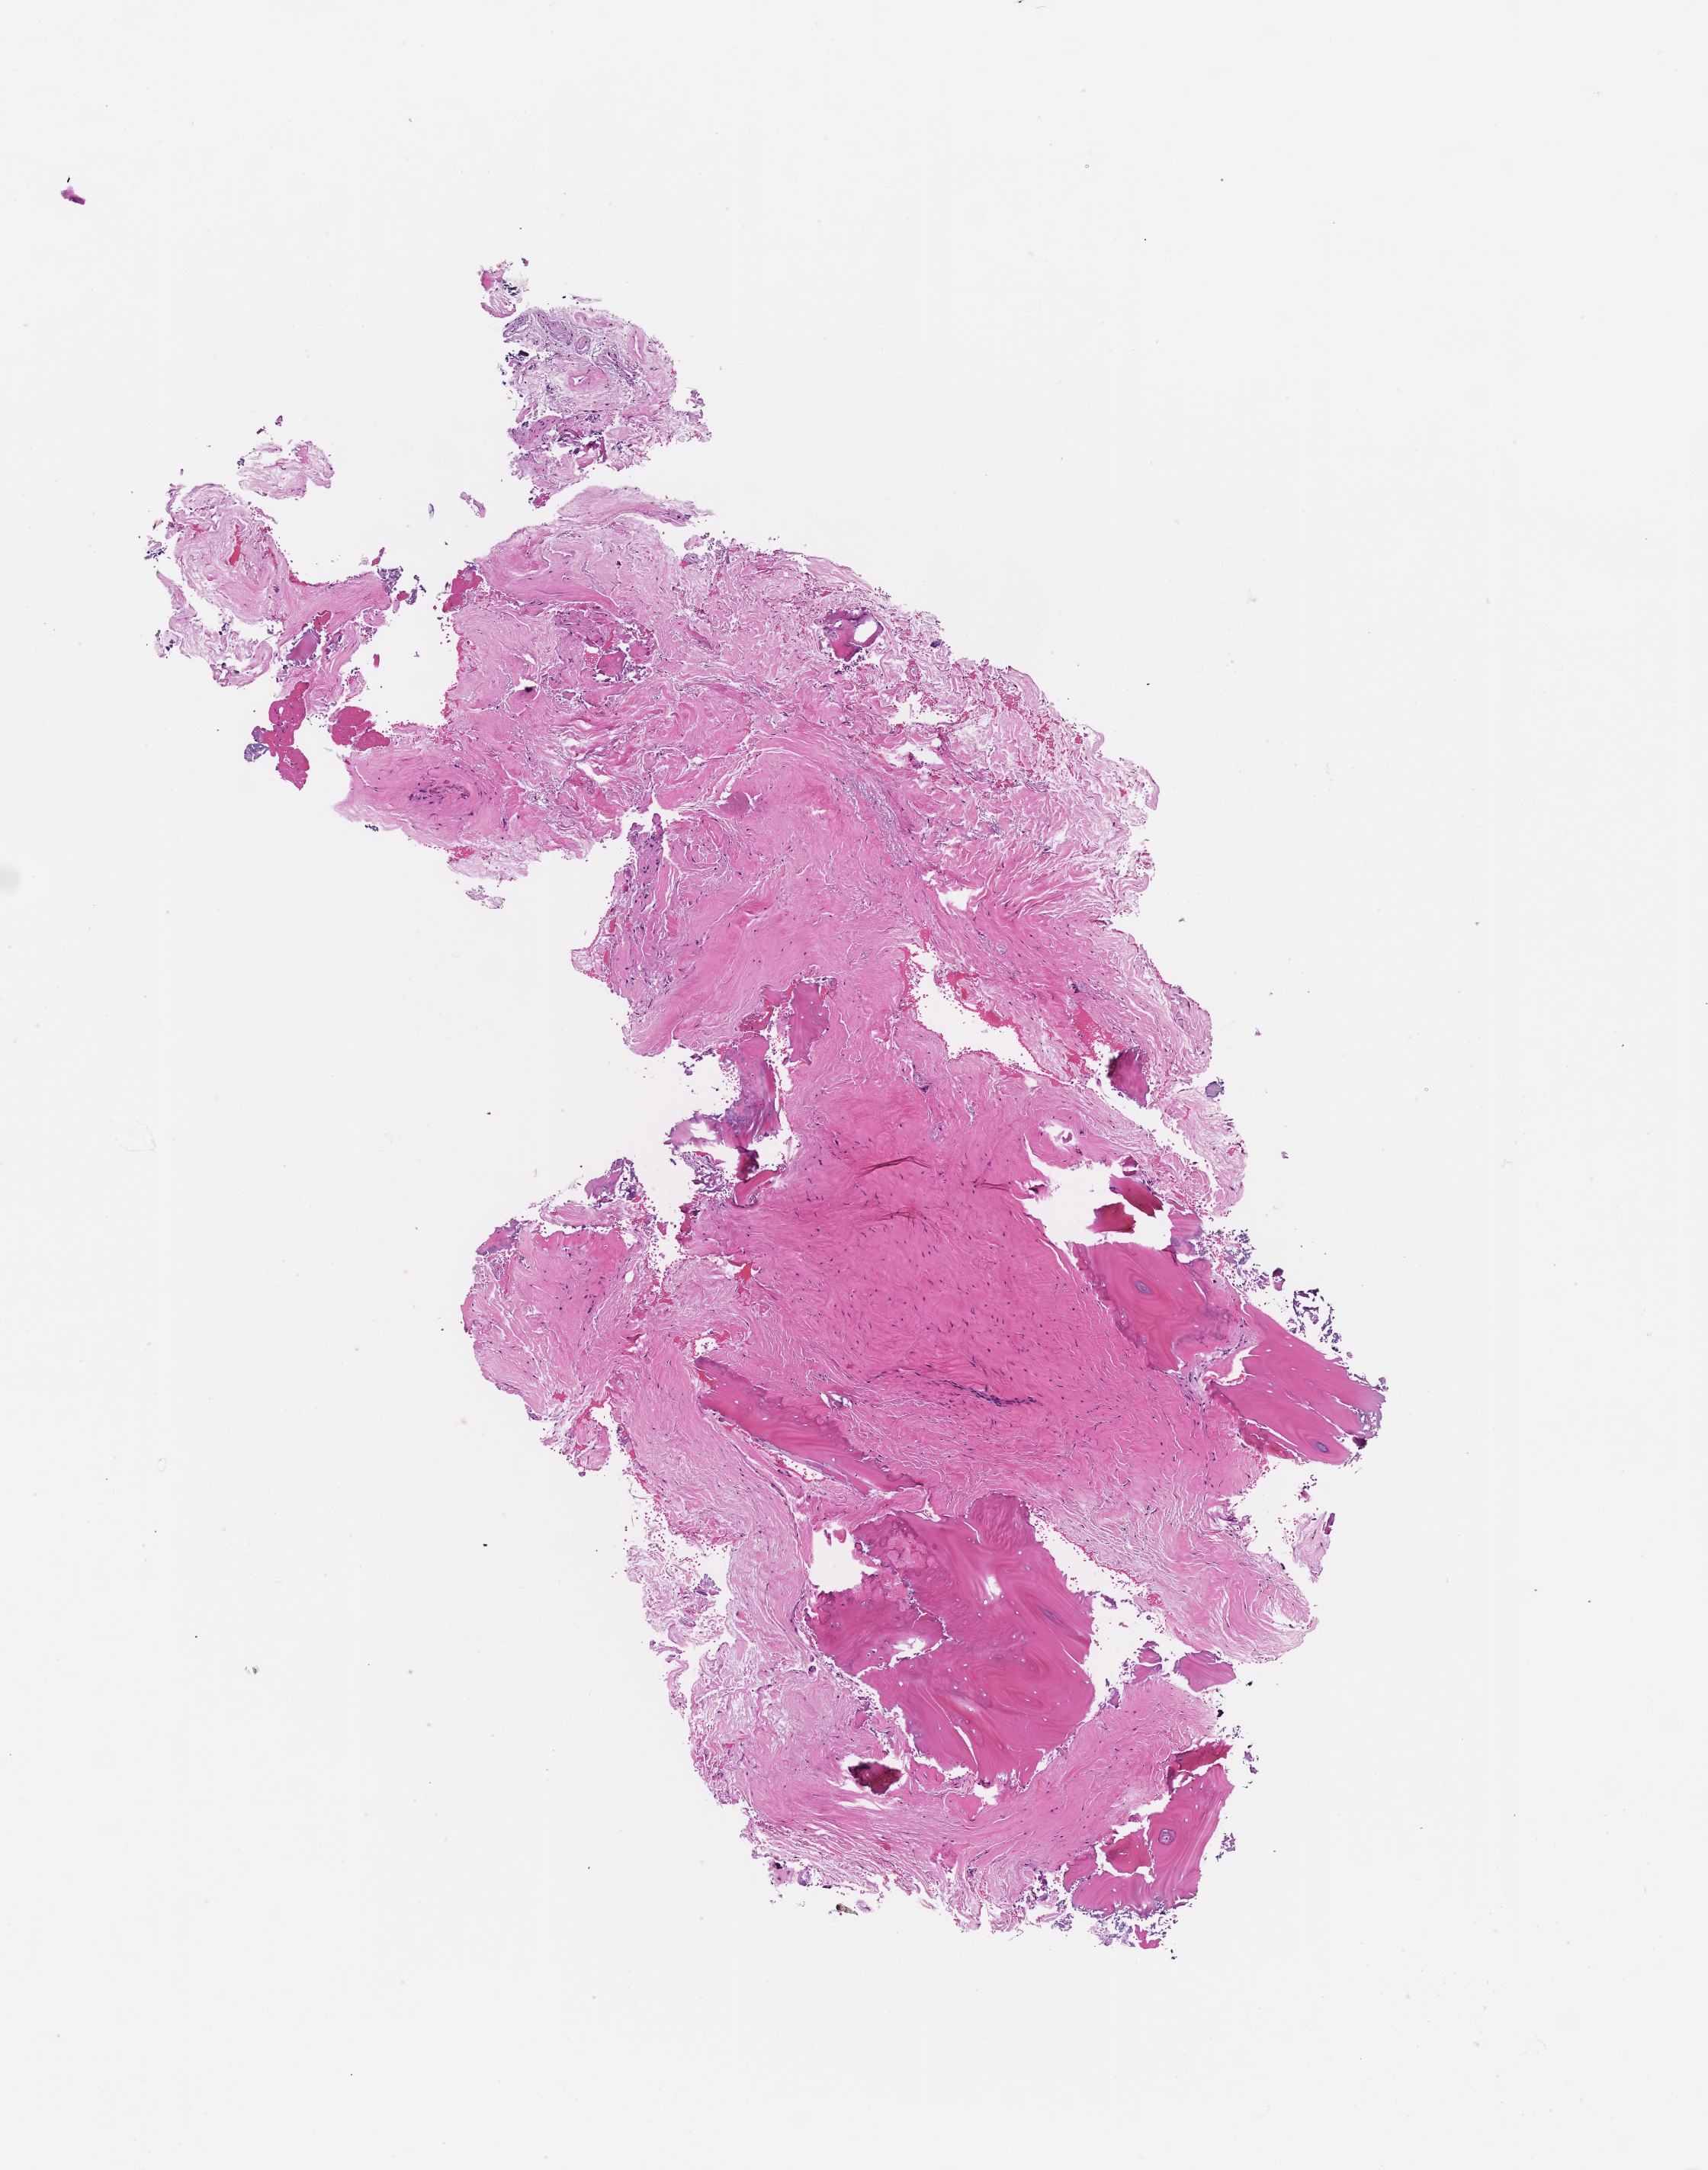
H&E whole-slide image, shown as a low-resolution overview of the whole scanned area (about 4.5 x 5.7 mm). FFPE section. Tissue site: bone marrow. Collected at baseline (before treatment). Female patient.
From a patient with: Plasma Cell Myeloma.